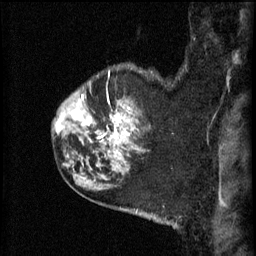
Breast MRI (dynamic contrast-enhanced), one sagittal slice; slice 49 of 60 in the series (ordered by position); 3 images stored at this slice position (order not interpretable as contrast timing); 1.5 T; TE 4.2 ms, TR 11 ms; 2.3 mm slice thickness; 256 × 256 image matrix, field of view 180 × 180 mm. Patient: female, 52 years.
Annotated regions visible in this slice (semi-automatically segmented with operator editing):
- analysis volume of interest (the breast-tissue region the enhancement analysis was run in; not a lesion): bounding box (x1, y1, x2, y2) in pixels: (86, 82, 152, 157)
- tumour enhancement mask (voxels above the 70 % enhancement threshold inside the analysis volume of interest): (99, 110, 129, 153)